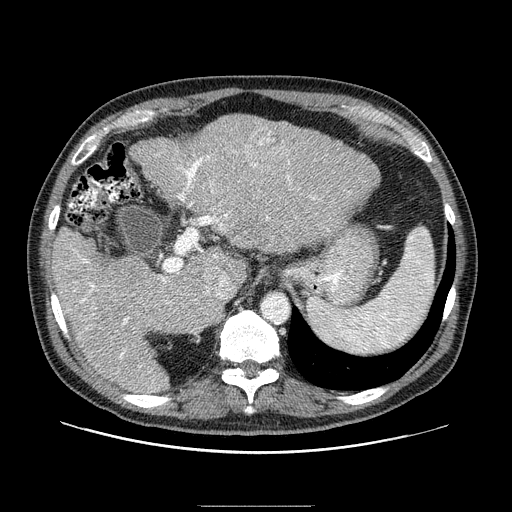
Contrast-enhanced abdominal CT (liver protocol), one axial slice; slice 58 of 99 in the series (ordered by position); 100 kVp; one of 2 acquisitions stored at this slice position; soft-tissue window (W 400 / L 40 HU); 512 × 512 image matrix, field of view 400 × 400 mm. From the clinical record (not read from this slice): diagnosis: hepatocellular carcinoma (patient treated with transarterial chemoembolisation; whether this scan precedes or follows treatment is not stated here); TNM stage (as recorded): Stage-II; Child-Pugh class: A; tumour differentiation: well differentiated.
Outlined on this slice (semi-automatic segmentation, software-assisted and operator-edited):
- liver parenchyma outside the tumour (the mass and vessels are separate outlines, so this box may not span the whole liver): box from (x=52, y=114) to (x=380, y=392) px
- mass: (x=243, y=127)–(x=289, y=173)
- liver vessels: (x=73, y=151)–(x=350, y=382)